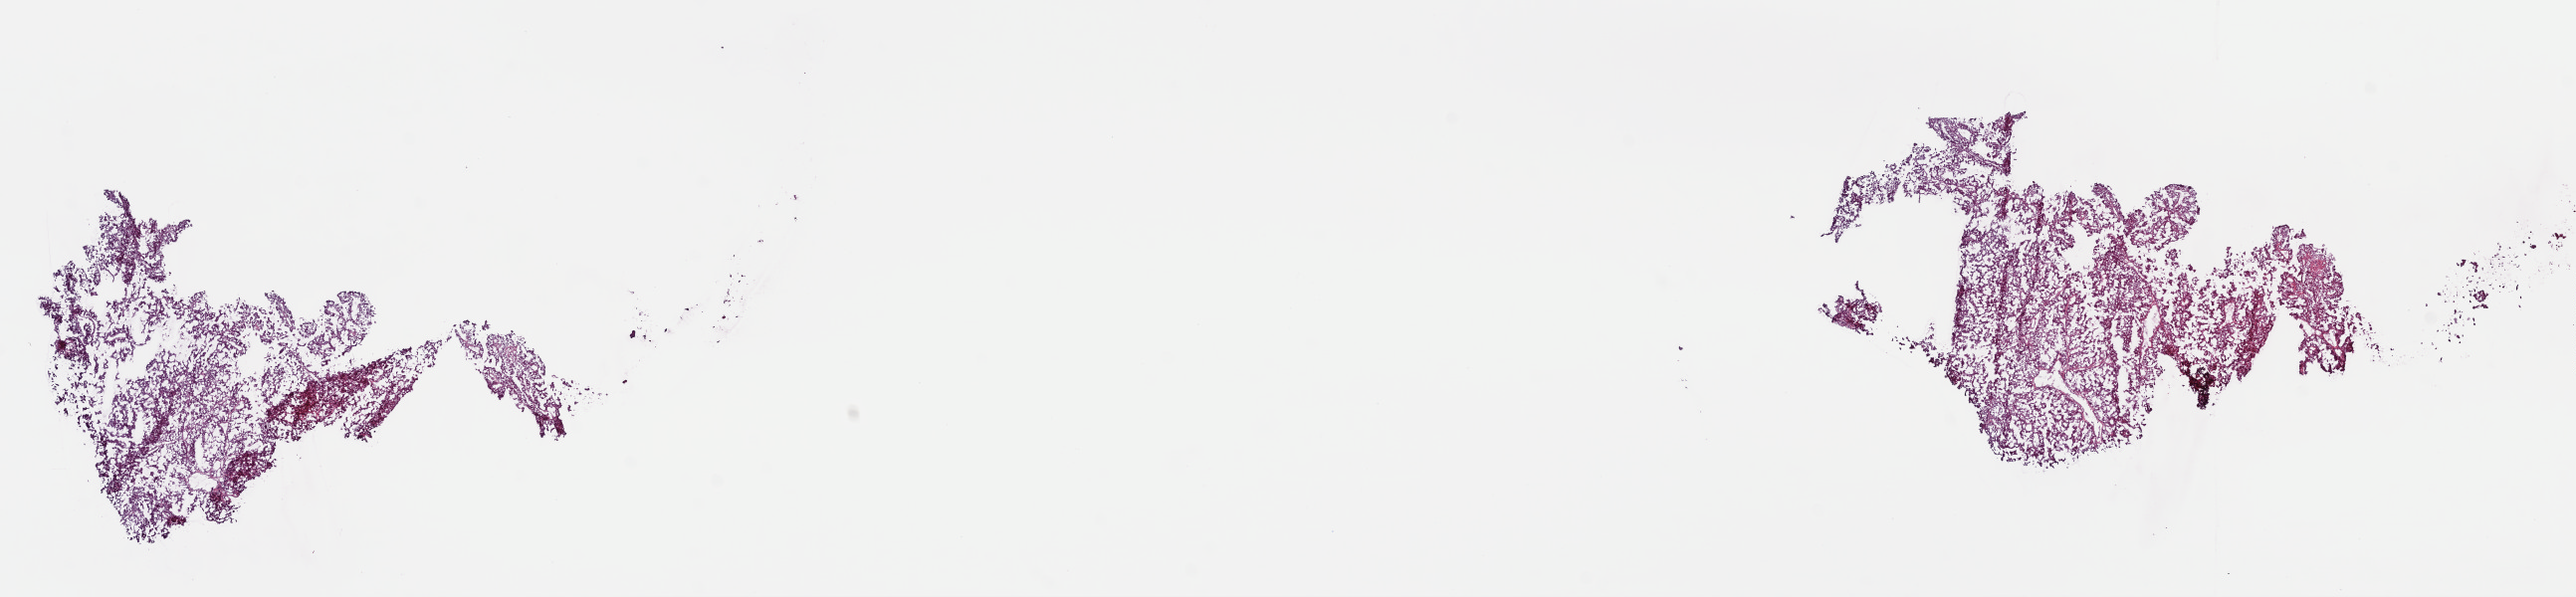
H&E whole-slide image — low-resolution overview of the scanned area, about 20.3 x 4.7 mm (from a 40x scan); frozen section from the top of the tissue portion; kidney, primary tumour sample. Patient: male, age at initial diagnosis 59 years. Histologic grade: G4 (undifferentiated). Pathologist review of this section (percent, as recorded): tumour cells 95%, tumour nuclei 90%, normal cells 0%, stromal cells 5%, necrosis 0%. Inflammatory infiltration, as recorded: lymphocyte infiltration 0%, monocyte infiltration 0%, neutrophil infiltration 0%.
• laterality: right
• diagnosis: Clear cell adenocarcinoma, NOS
• lymph nodes positive (case pathology): 0 of 25 examined
• AJCC pathologic stage: IV